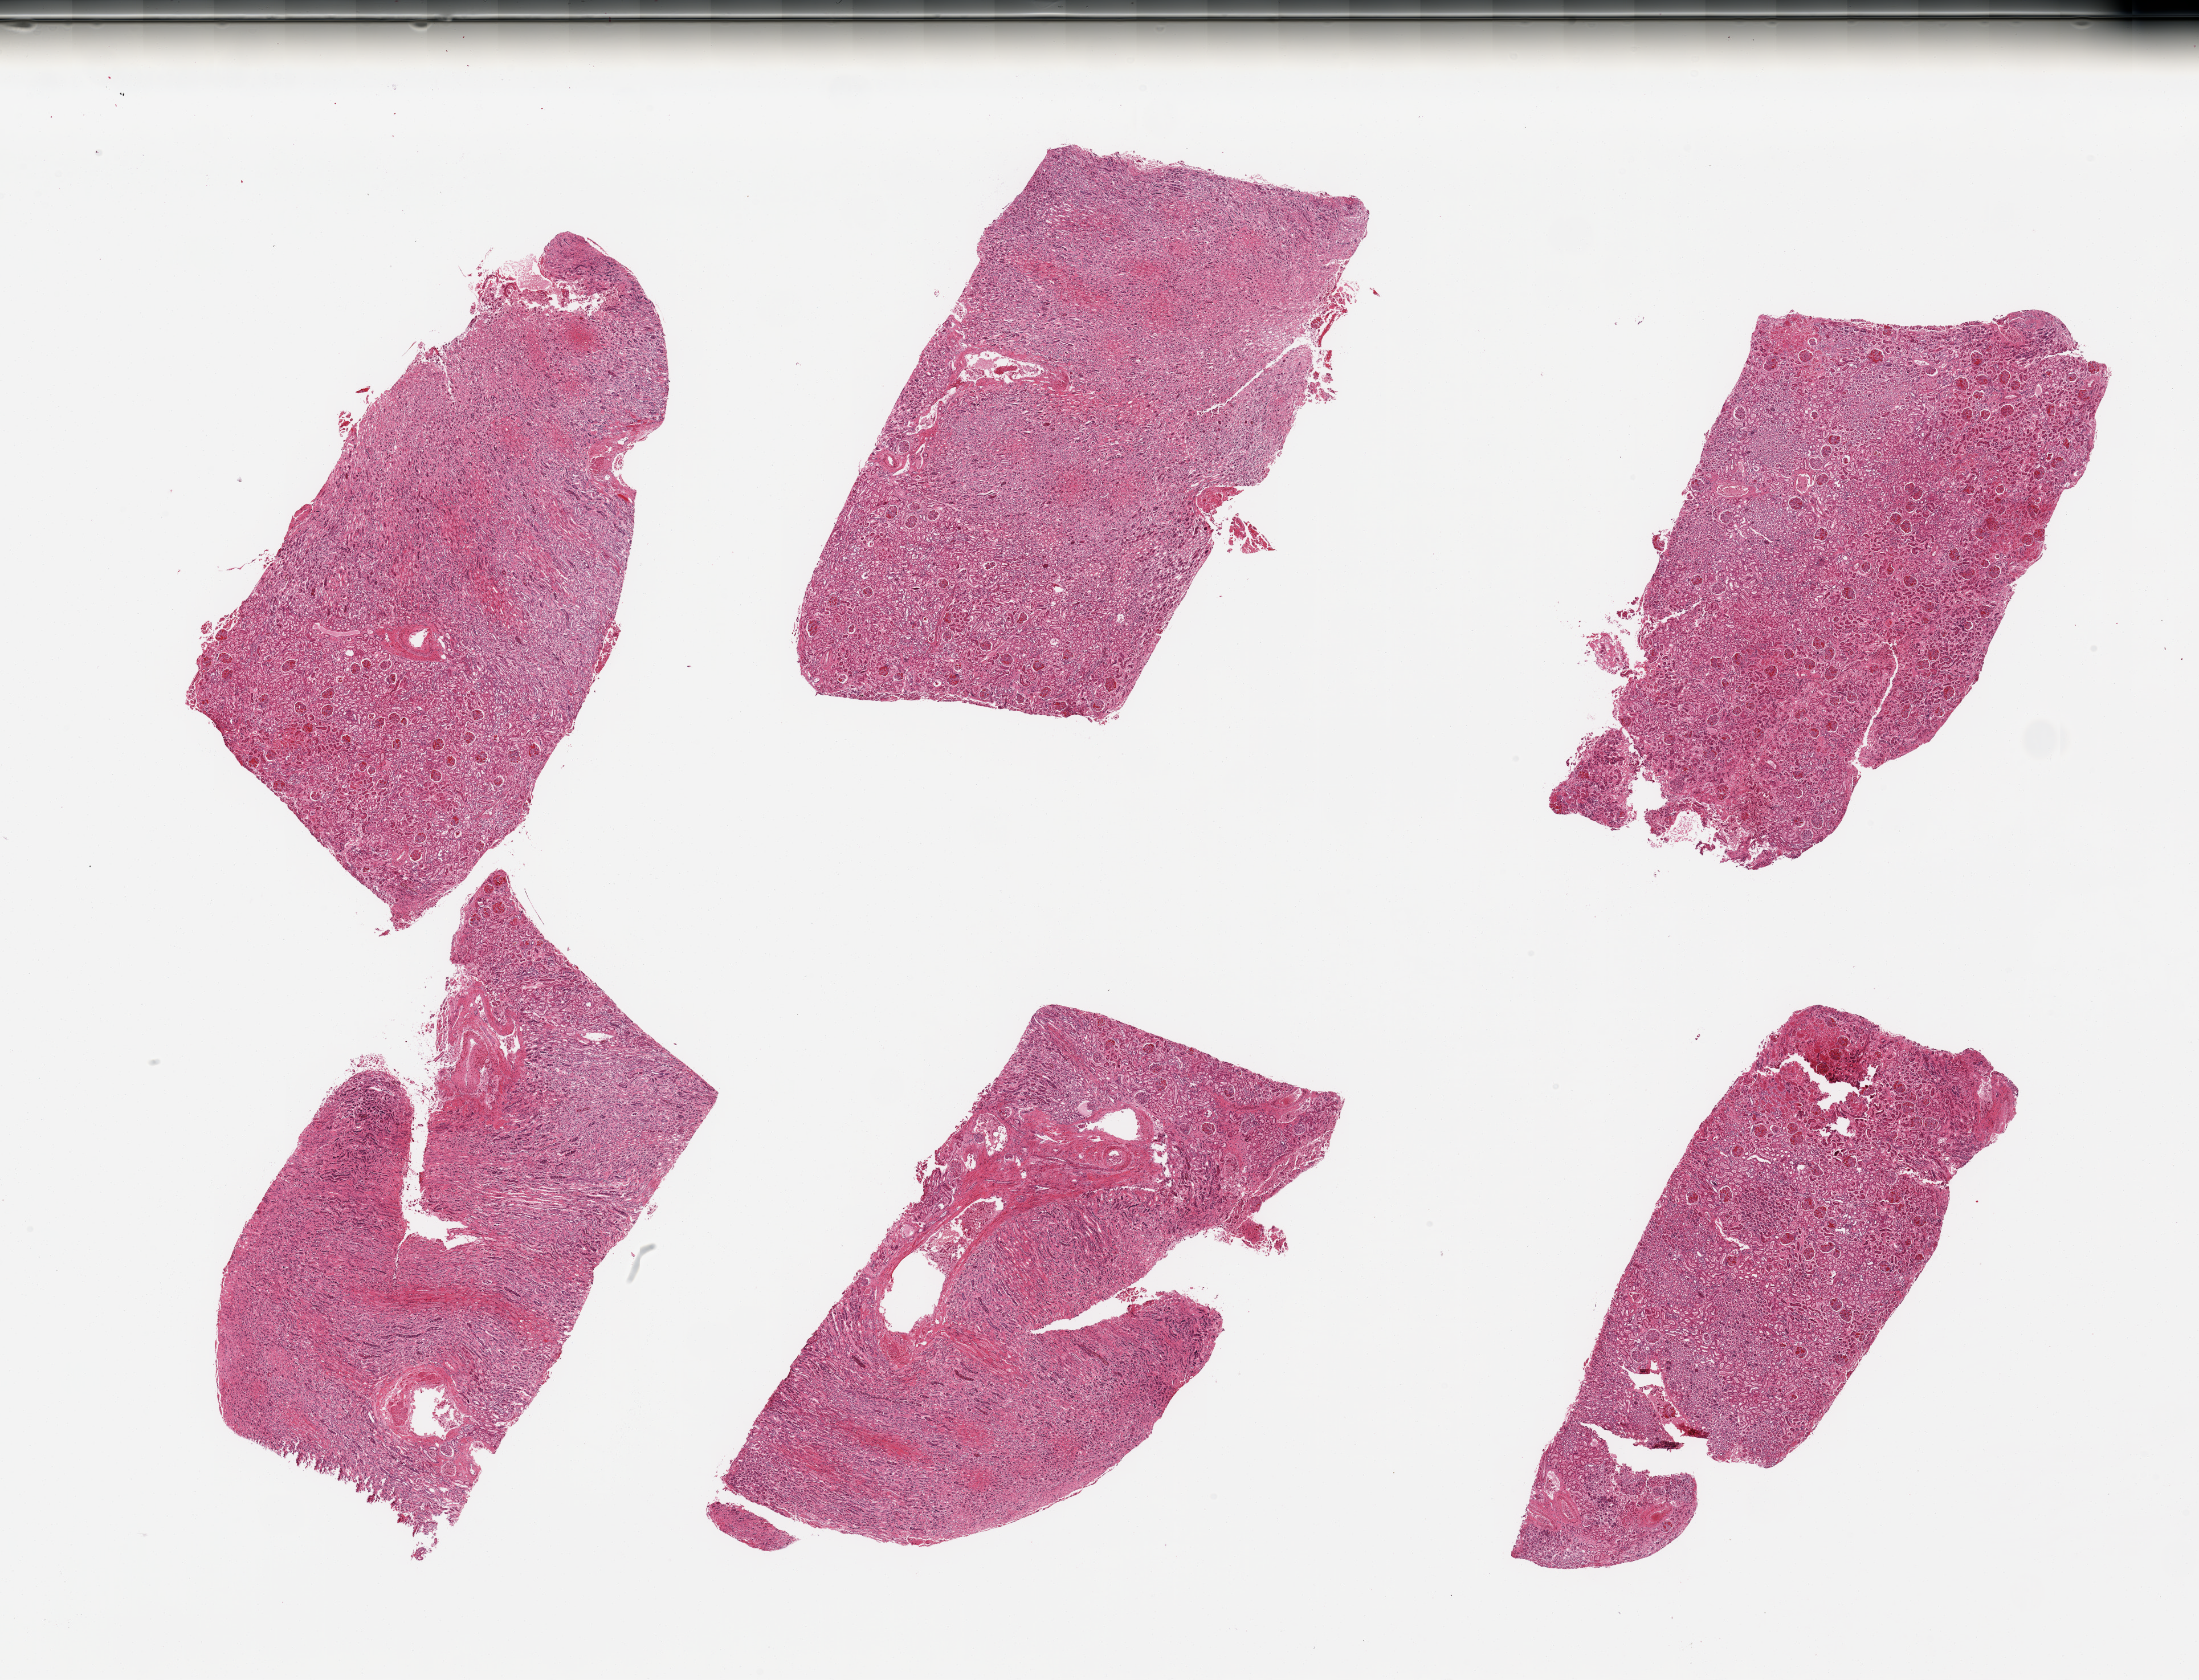
Digitized hematoxylin and eosin (H&E)-stained section, brightfield, whole scanned area (about 30.5 x 23.3 mm) shown as a low-resolution overview. PAXgene-fixed paraffin-embedded (PFPE) section. Target tissue: renal cortex. Donor tissue sample. Male donor.
• reviewer comment on this tissue sample: 6 pieces, glomeruli present